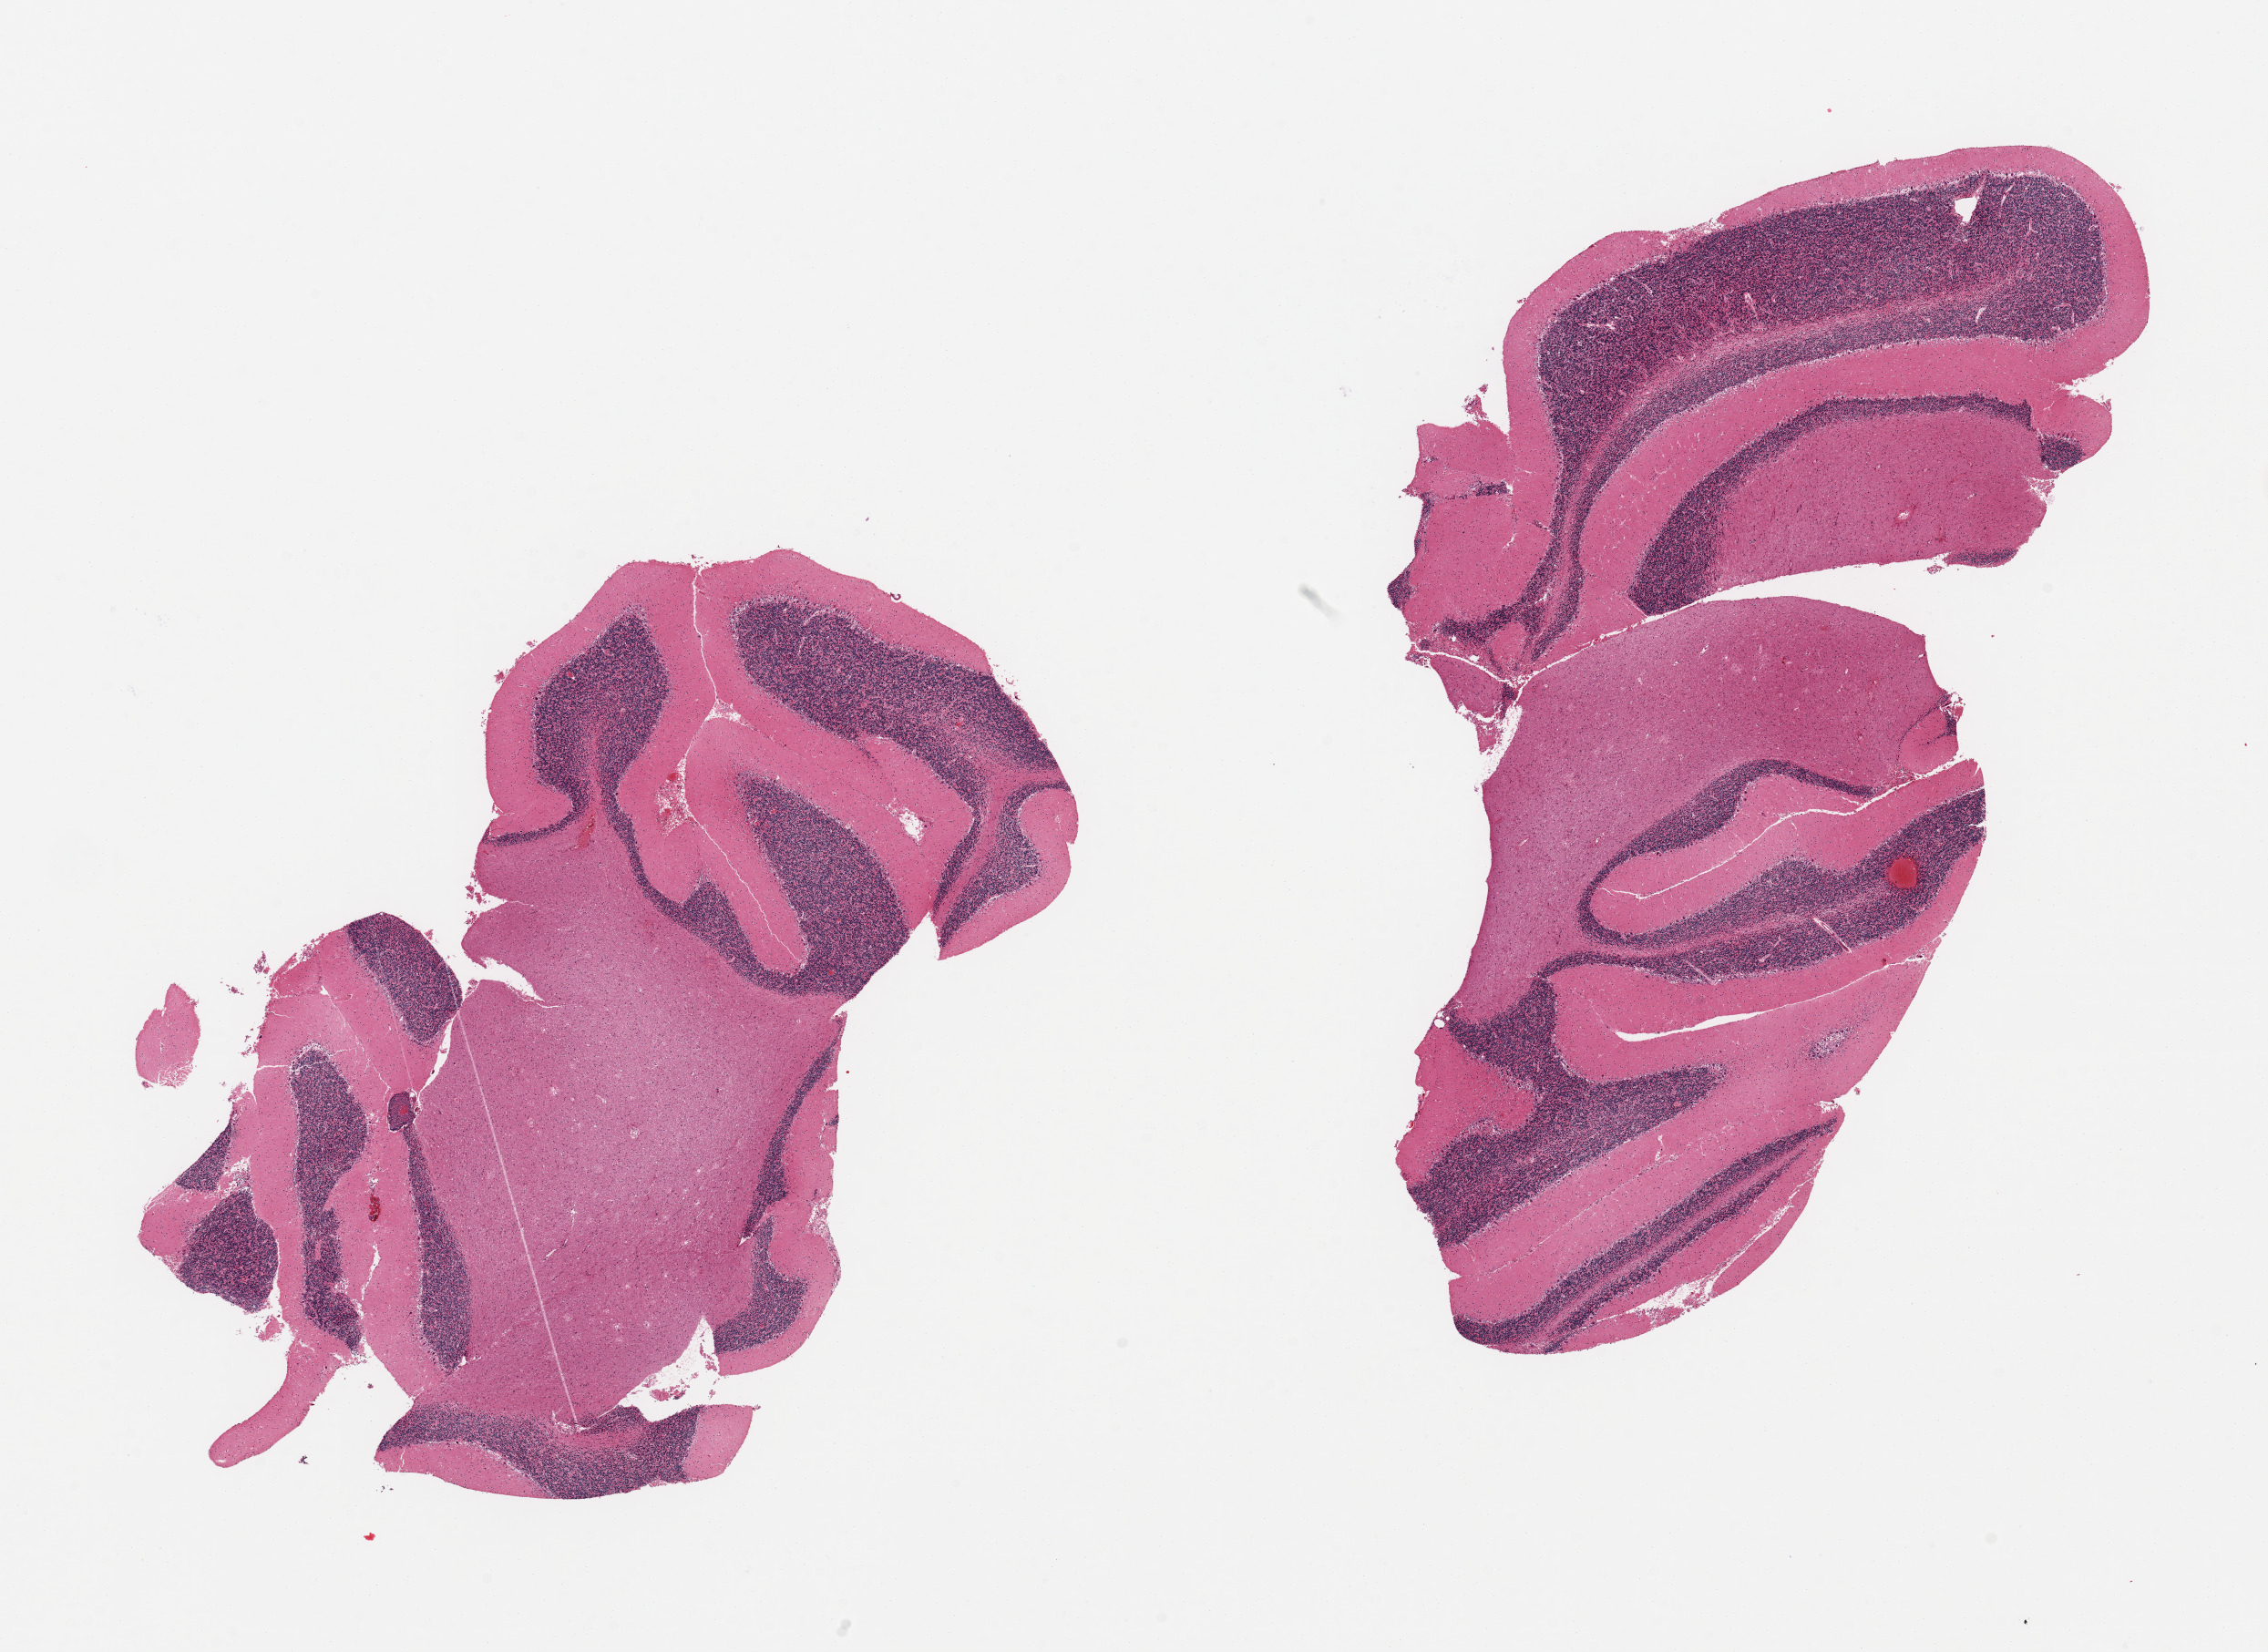
Digitized hematoxylin and eosin (H&E)-stained section — whole scanned area (about 19.7 x 14.3 mm) shown as a low-resolution overview. PAXgene-fixed paraffin-embedded (PFPE) section. Sampled site (target tissue): cerebellum. Donor tissue sample. Male donor.
Pathologist's review note for this sample: 2 pieces, no abnormalities.